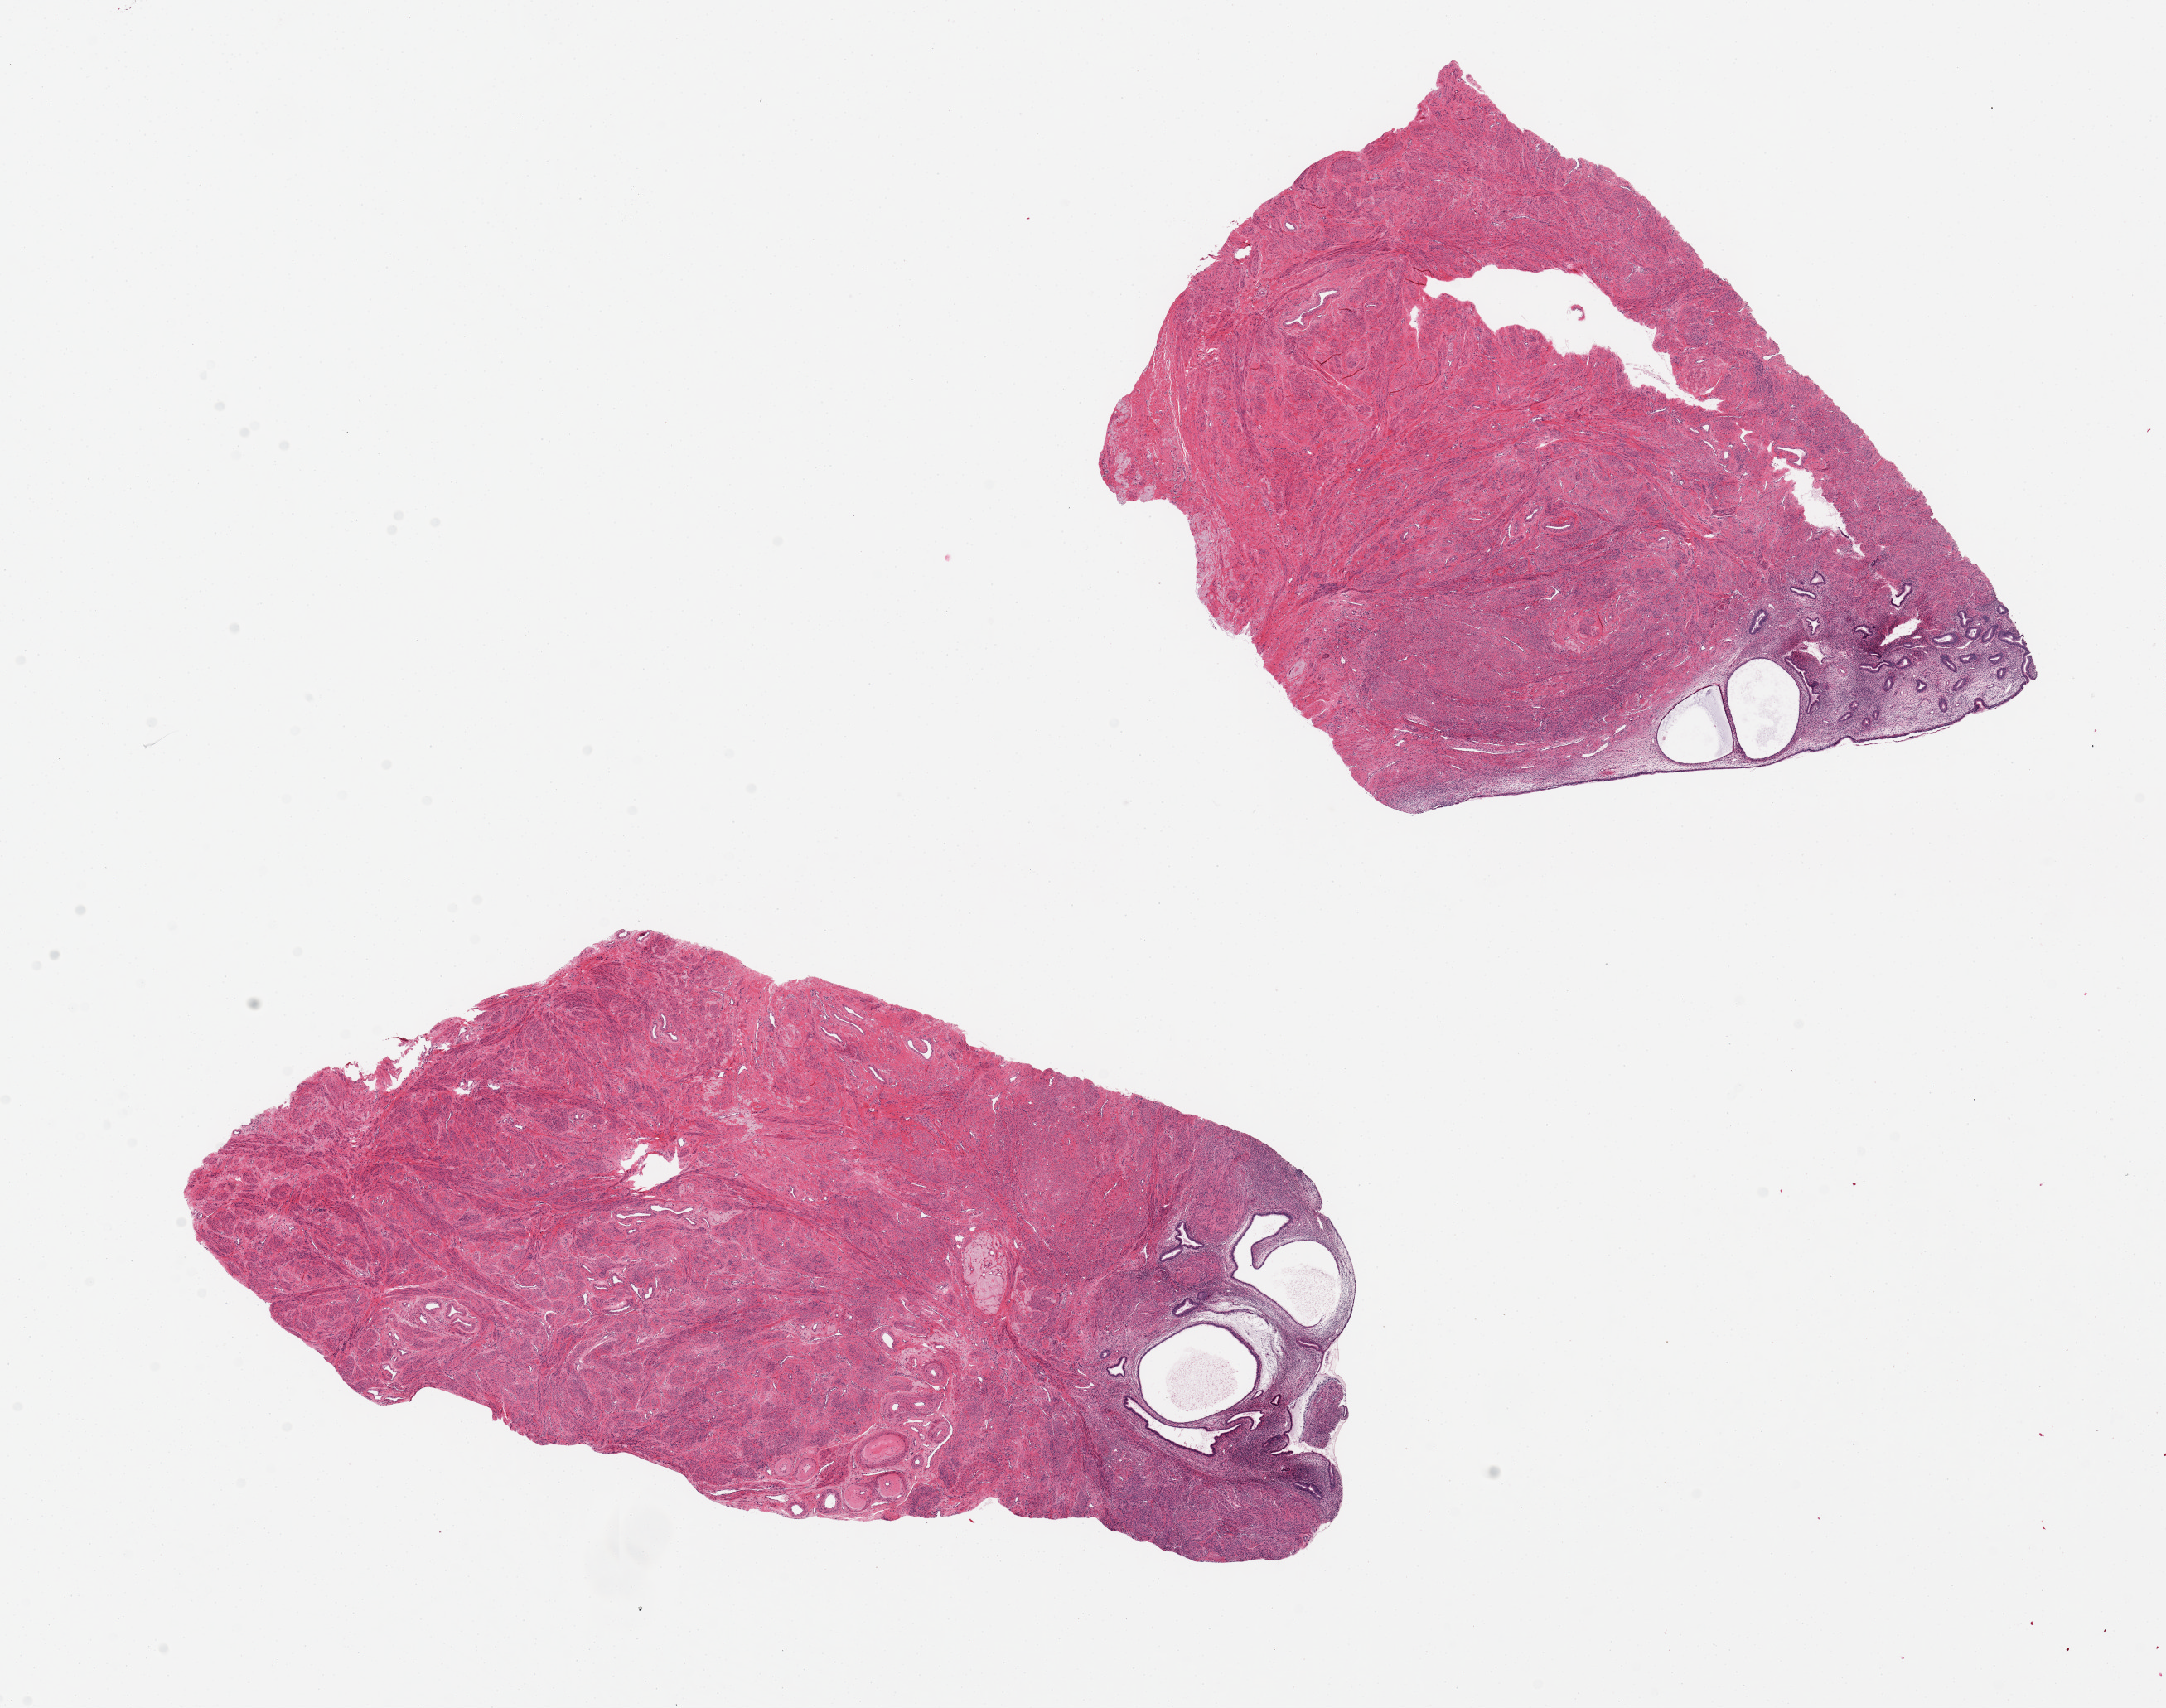
Hematoxylin and eosin (H&E) whole-slide image, brightfield — low-resolution overview of the scanned area, about 20.7 x 16.3 mm; PAXgene-fixed, paraffin-embedded tissue; section of uterus (target tissue); donor tissue sample. Female donor.
Pathologist's review note for this sample: 2 pieces, 11.5x5 & 8x6mm; cystic atrophy/weakly proliferative endometrium, up to ~2mm thick.